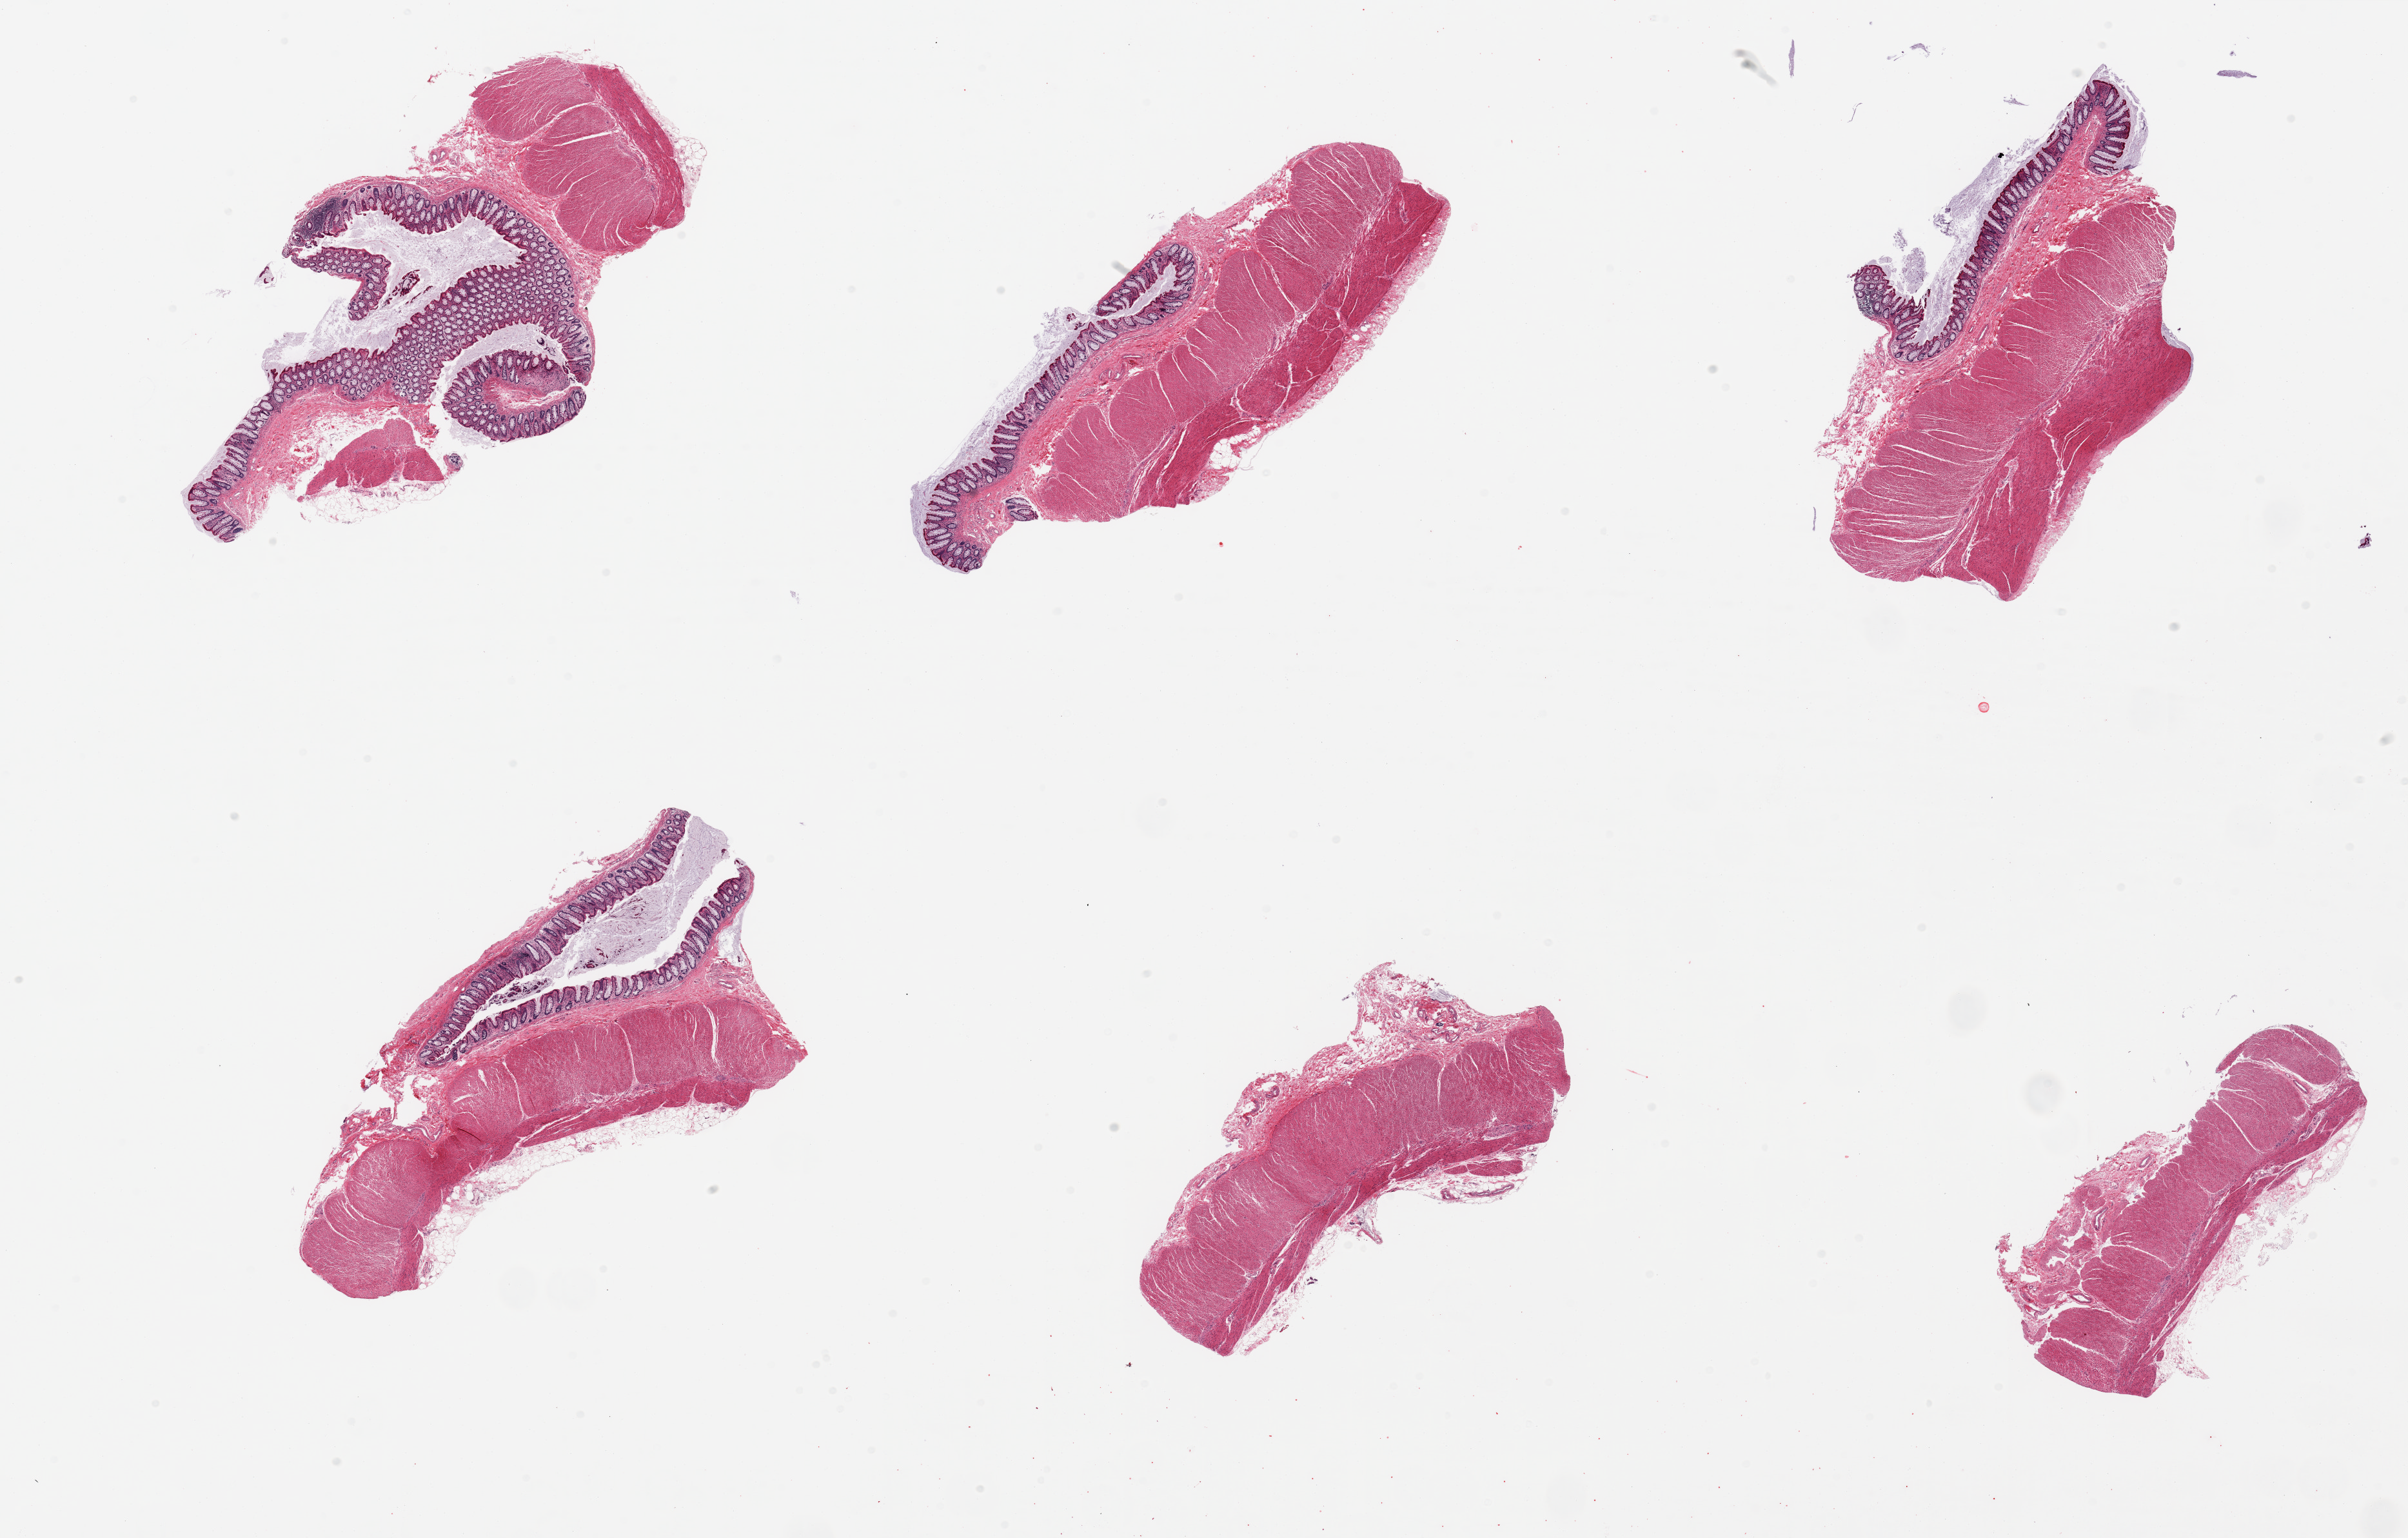
Haematoxylin and eosin whole-slide image — low-resolution overview of the scanned area, about 29.5 x 18.9 mm. PAXgene-fixed paraffin-embedded (PFPE) section. Target tissue: transverse colon. Donor tissue sample. Donor sex: male.
Review note (as recorded): 6 pieces, well preserved mucosa, ~10% of thickness.